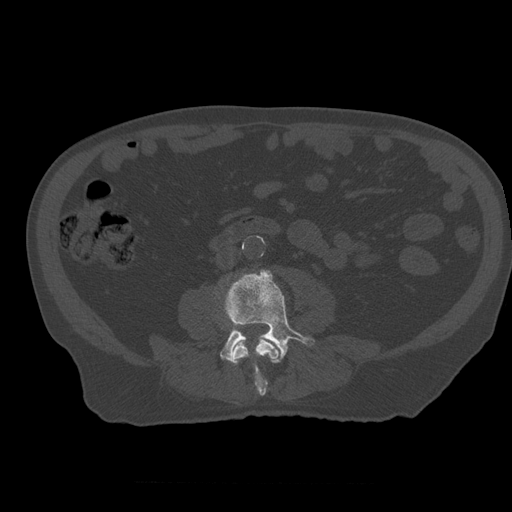
CT including the spine, one axial slice. Slice 174 of 399 in the series (ordered by position). 120 kVp. Bone window (W 1800 / L 400 HU). 1.25 mm slice thickness. 512 × 512 image matrix. Patient age 73 years. From the clinical record (not read from this slice): primary cancer: prostate.
Annotated regions visible in this slice (semi-automatic segmentation, software-assisted and operator-edited):
- L3 vertebra: bounding box <231,336,281,396> (left, top, right, bottom; pixels)
- L4 vertebra: <221,269,315,363>